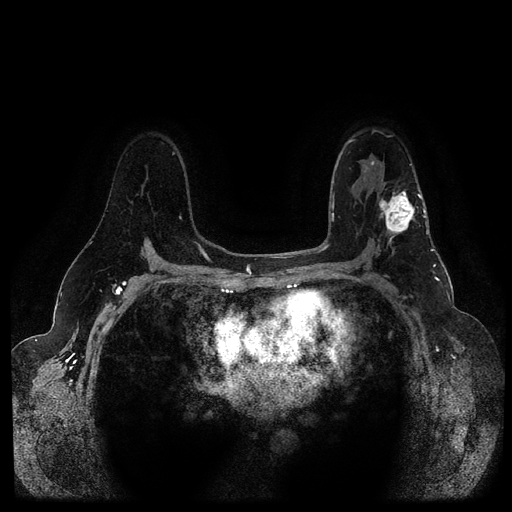
Breast MRI (dynamic contrast-enhanced, multi-phase), one axial slice. Slice 70 of 116 in the series (ordered by position). Dynamic contrast-enhanced series, time point 2 of 5 at this slice position (early post-contrast). 1.5 T. TE 2.6 ms, TR 5.3 ms. 2 mm slice thickness. 512 × 512 image matrix. Female patient, age 54 years.
Annotated regions visible in this slice (semi-automatically segmented with operator editing):
- breast lesion (labelled 'tumour' in the annotation; benign lesions carry a separate 'benign' label): bounding box [x1, y1, x2, y2] px = [377, 186, 419, 243]